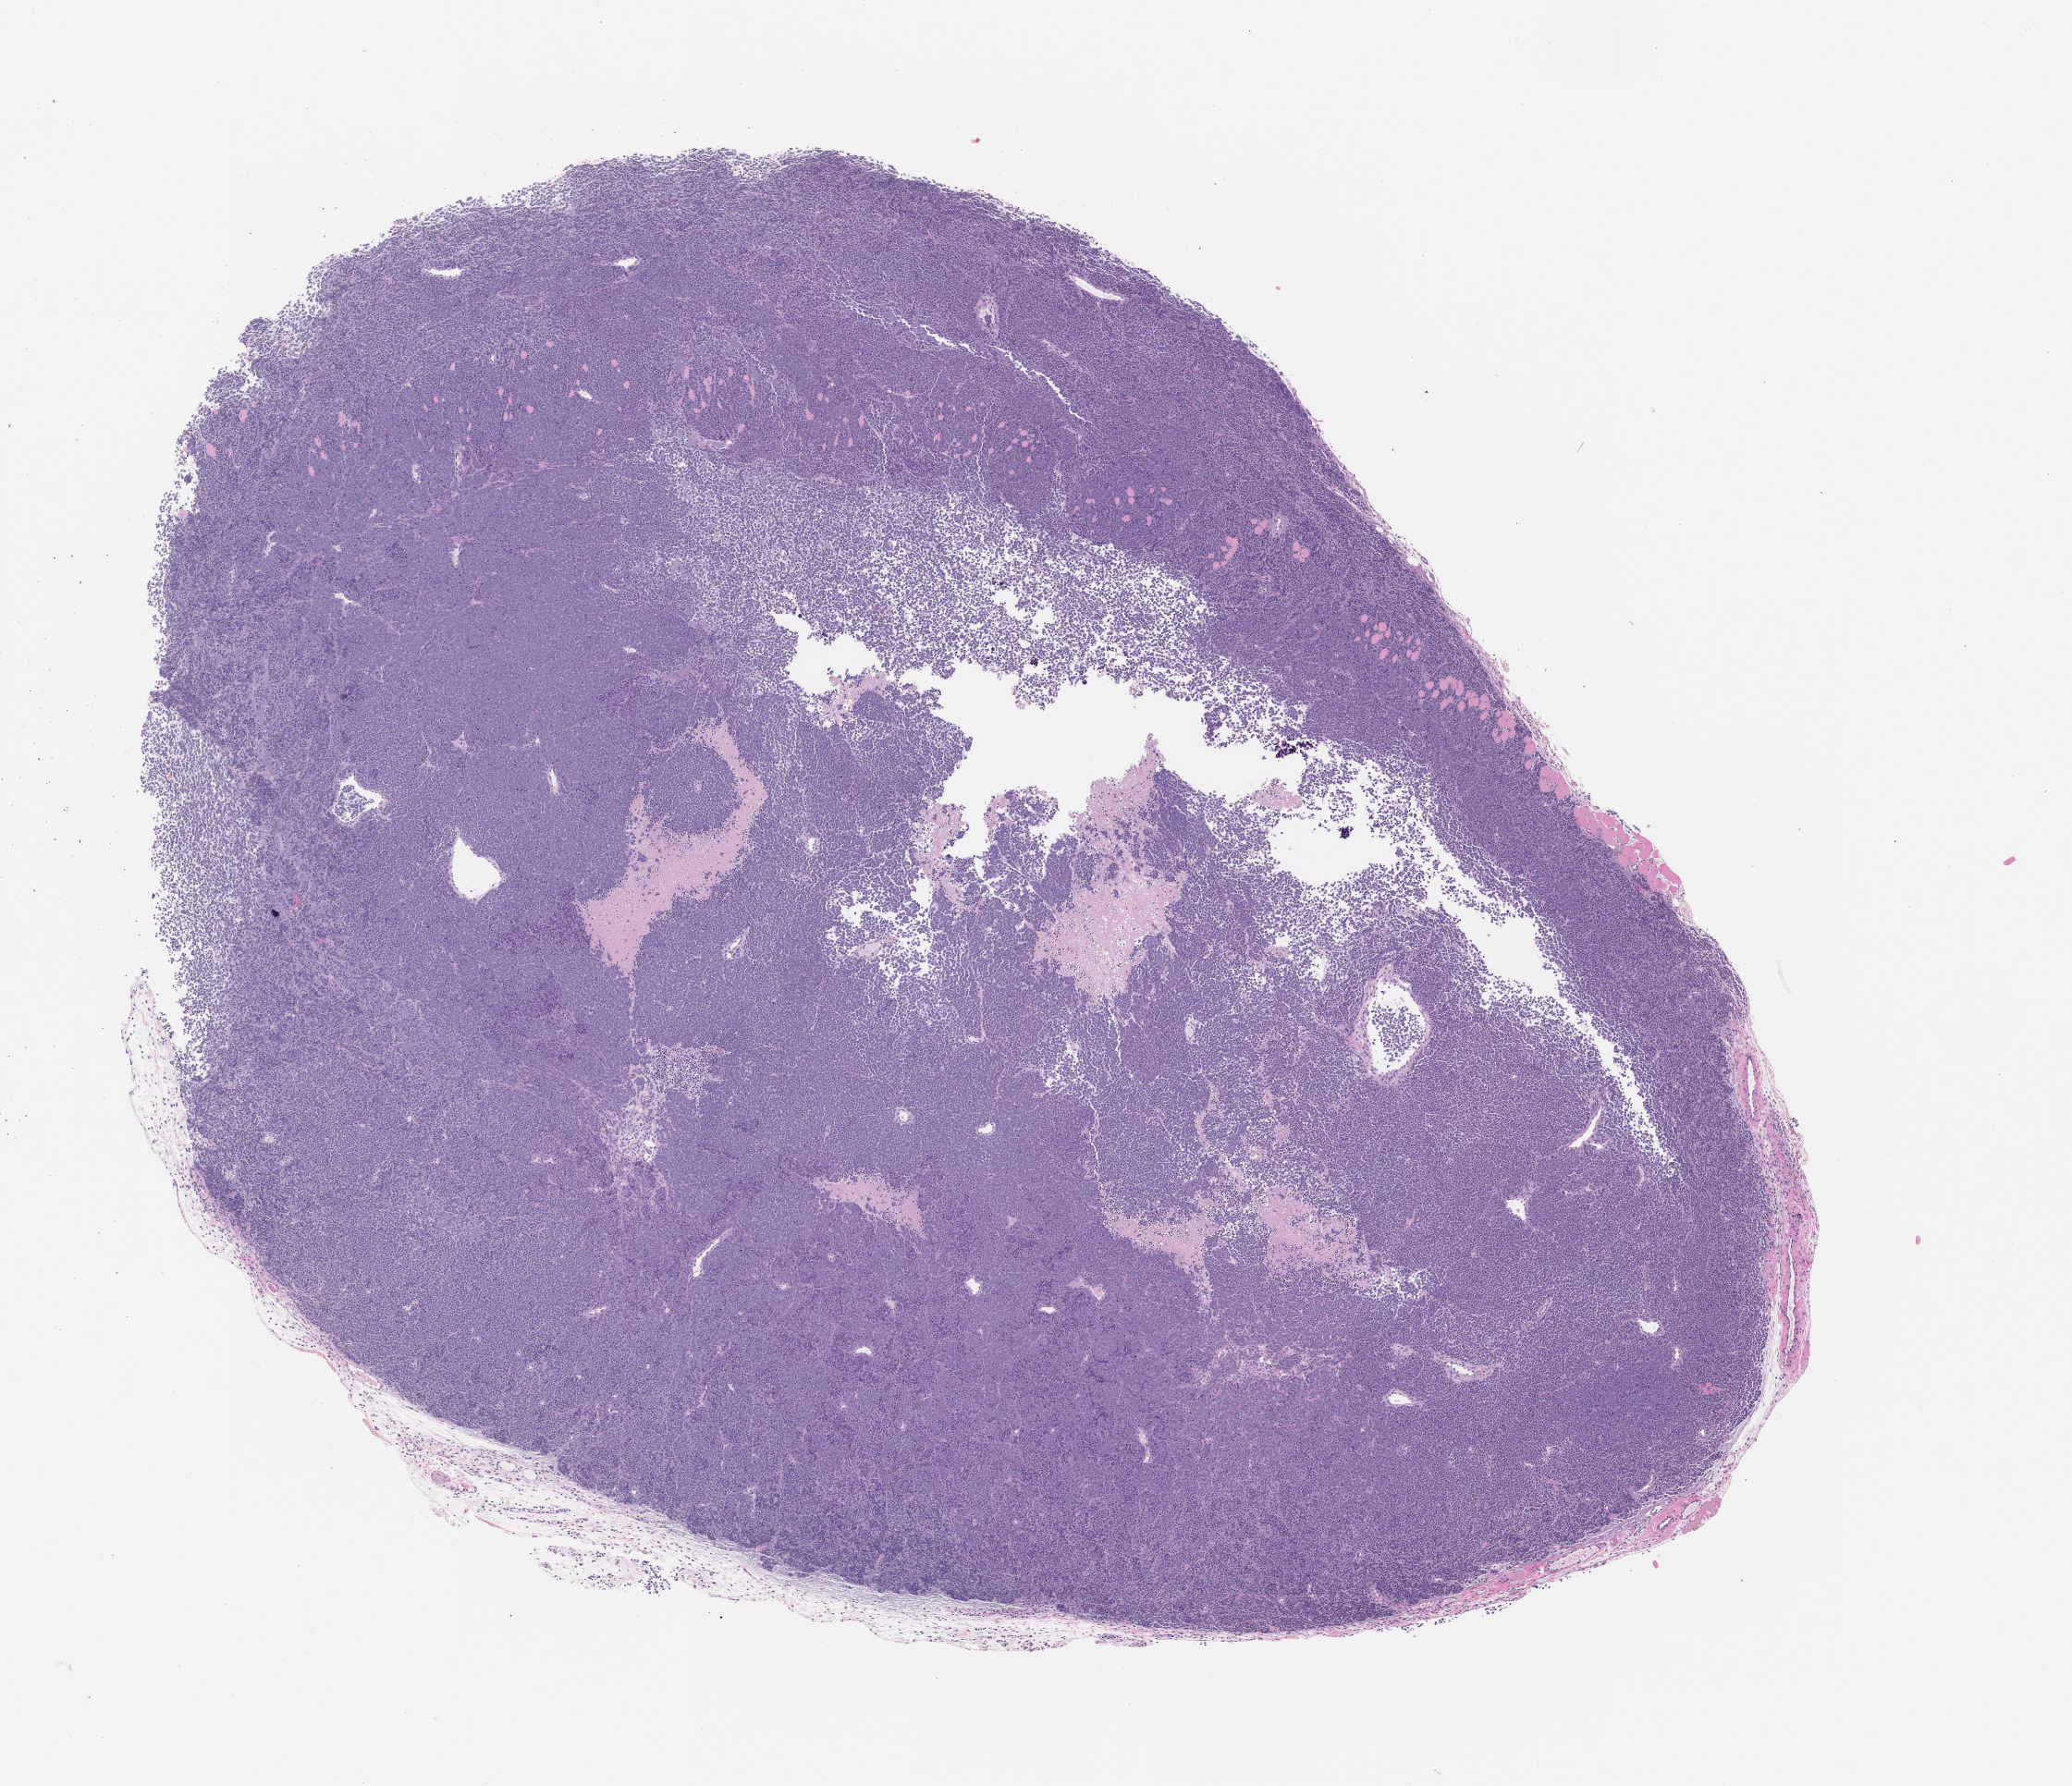
Whole-slide image, haematoxylin and eosin: patient-derived xenograft (human tumor grown in a mouse) — whole scanned area (about 9.0 x 7.8 mm) shown as a low-resolution overview. Formalin-fixed, paraffin-embedded (FFPE) tissue. Tumor site category: endocrine.
Originating patient diagnosis: Merkel Cell Carcinoma.